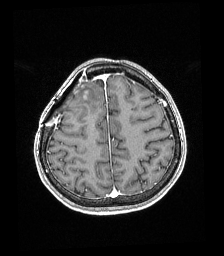
Brain MRI from a brain-tumour surgery series, one axial slice. T1-weighted post-contrast. 224 × 256 image matrix, field of view 219 × 250 mm. From the clinical record (not read from this slice): histopathology: Astrocytoma; WHO grade: 4; IDH mutation: yes; tumour location: Right superficial frontal.
Outlined on this slice (outlined manually by an expert reader):
- tumour: bounding box [x1, y1, x2, y2] px = [78, 90, 87, 98]